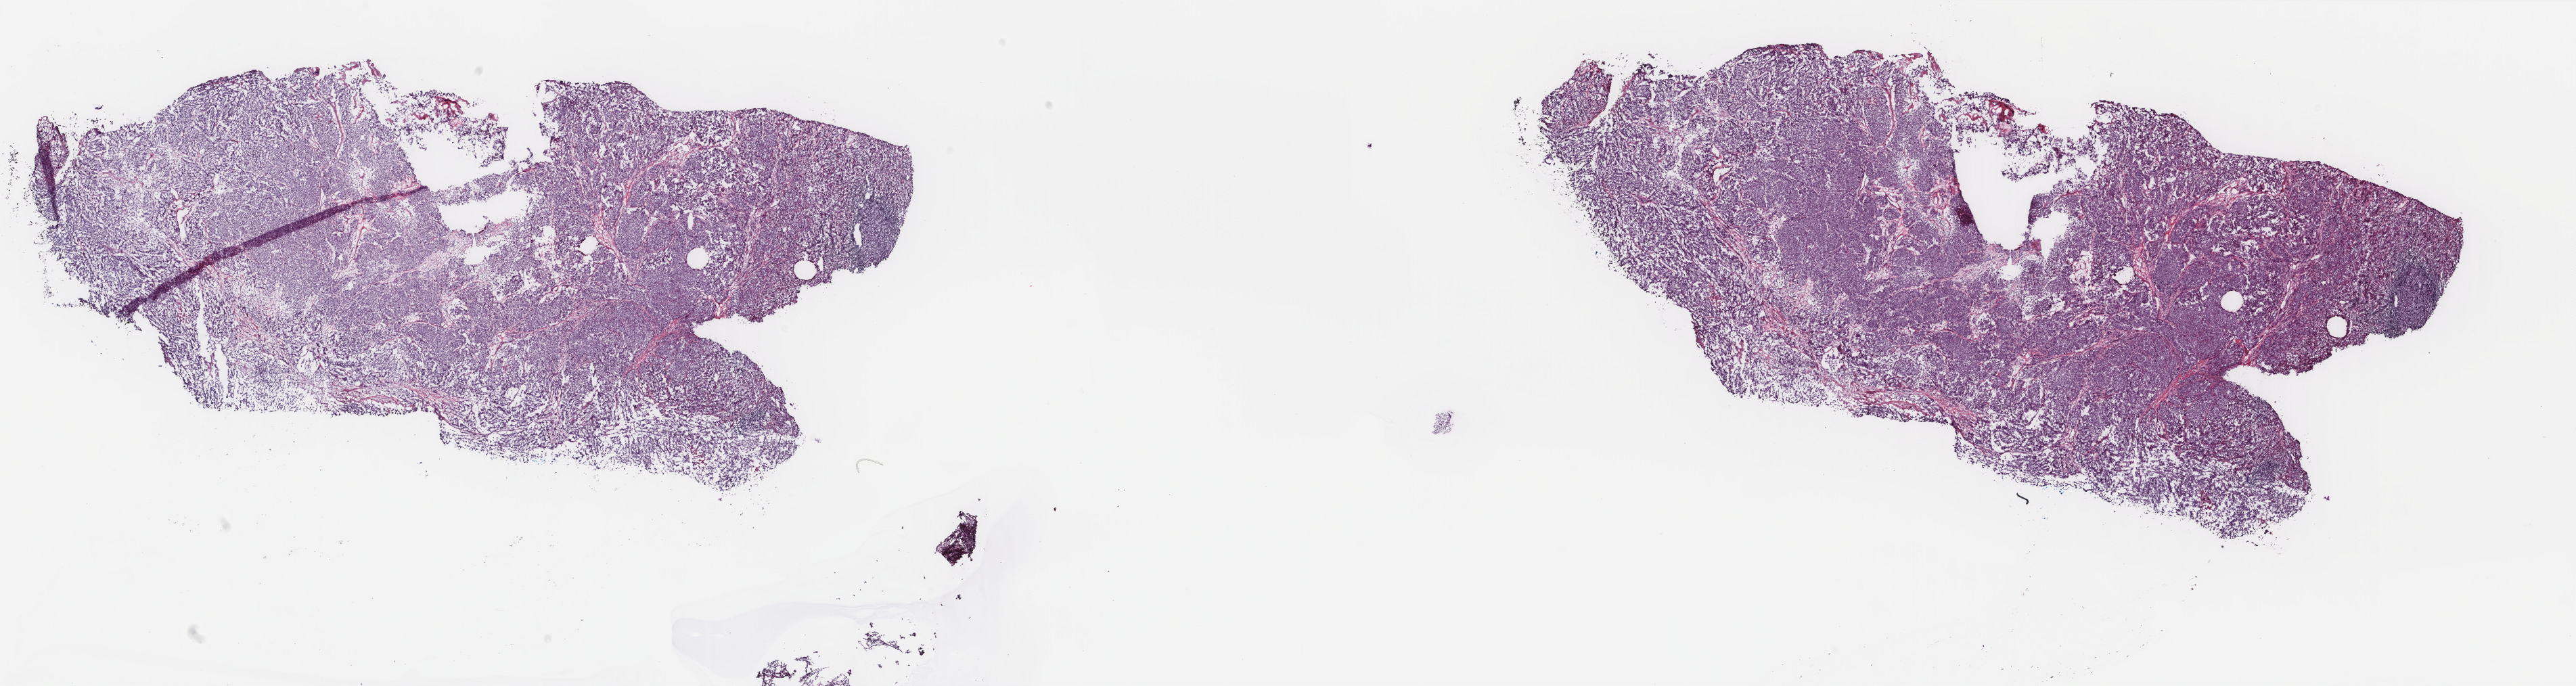
Whole-slide histology image, Hematoxylin and eosin (H&E) stained — low-resolution overview of the scanned area, about 30.2 x 8.0 mm (from a 40x scan); frozen section from the top of the tissue portion; metastatic tumour sample, sampled site: lymph nodes of axilla or arm. Female, age 57 years at initial diagnosis. Slide review estimates, as recorded: tumour cells 100%, tumour nuclei 96%, normal cells 0%, stromal cells 0%, necrosis 0%. Inflammatory infiltration, as recorded: lymphocyte infiltration 0%, monocyte infiltration 0%, neutrophil infiltration 0%.
This section: metastatic tumour tissue. Patient diagnosis: Malignant melanoma, NOS.